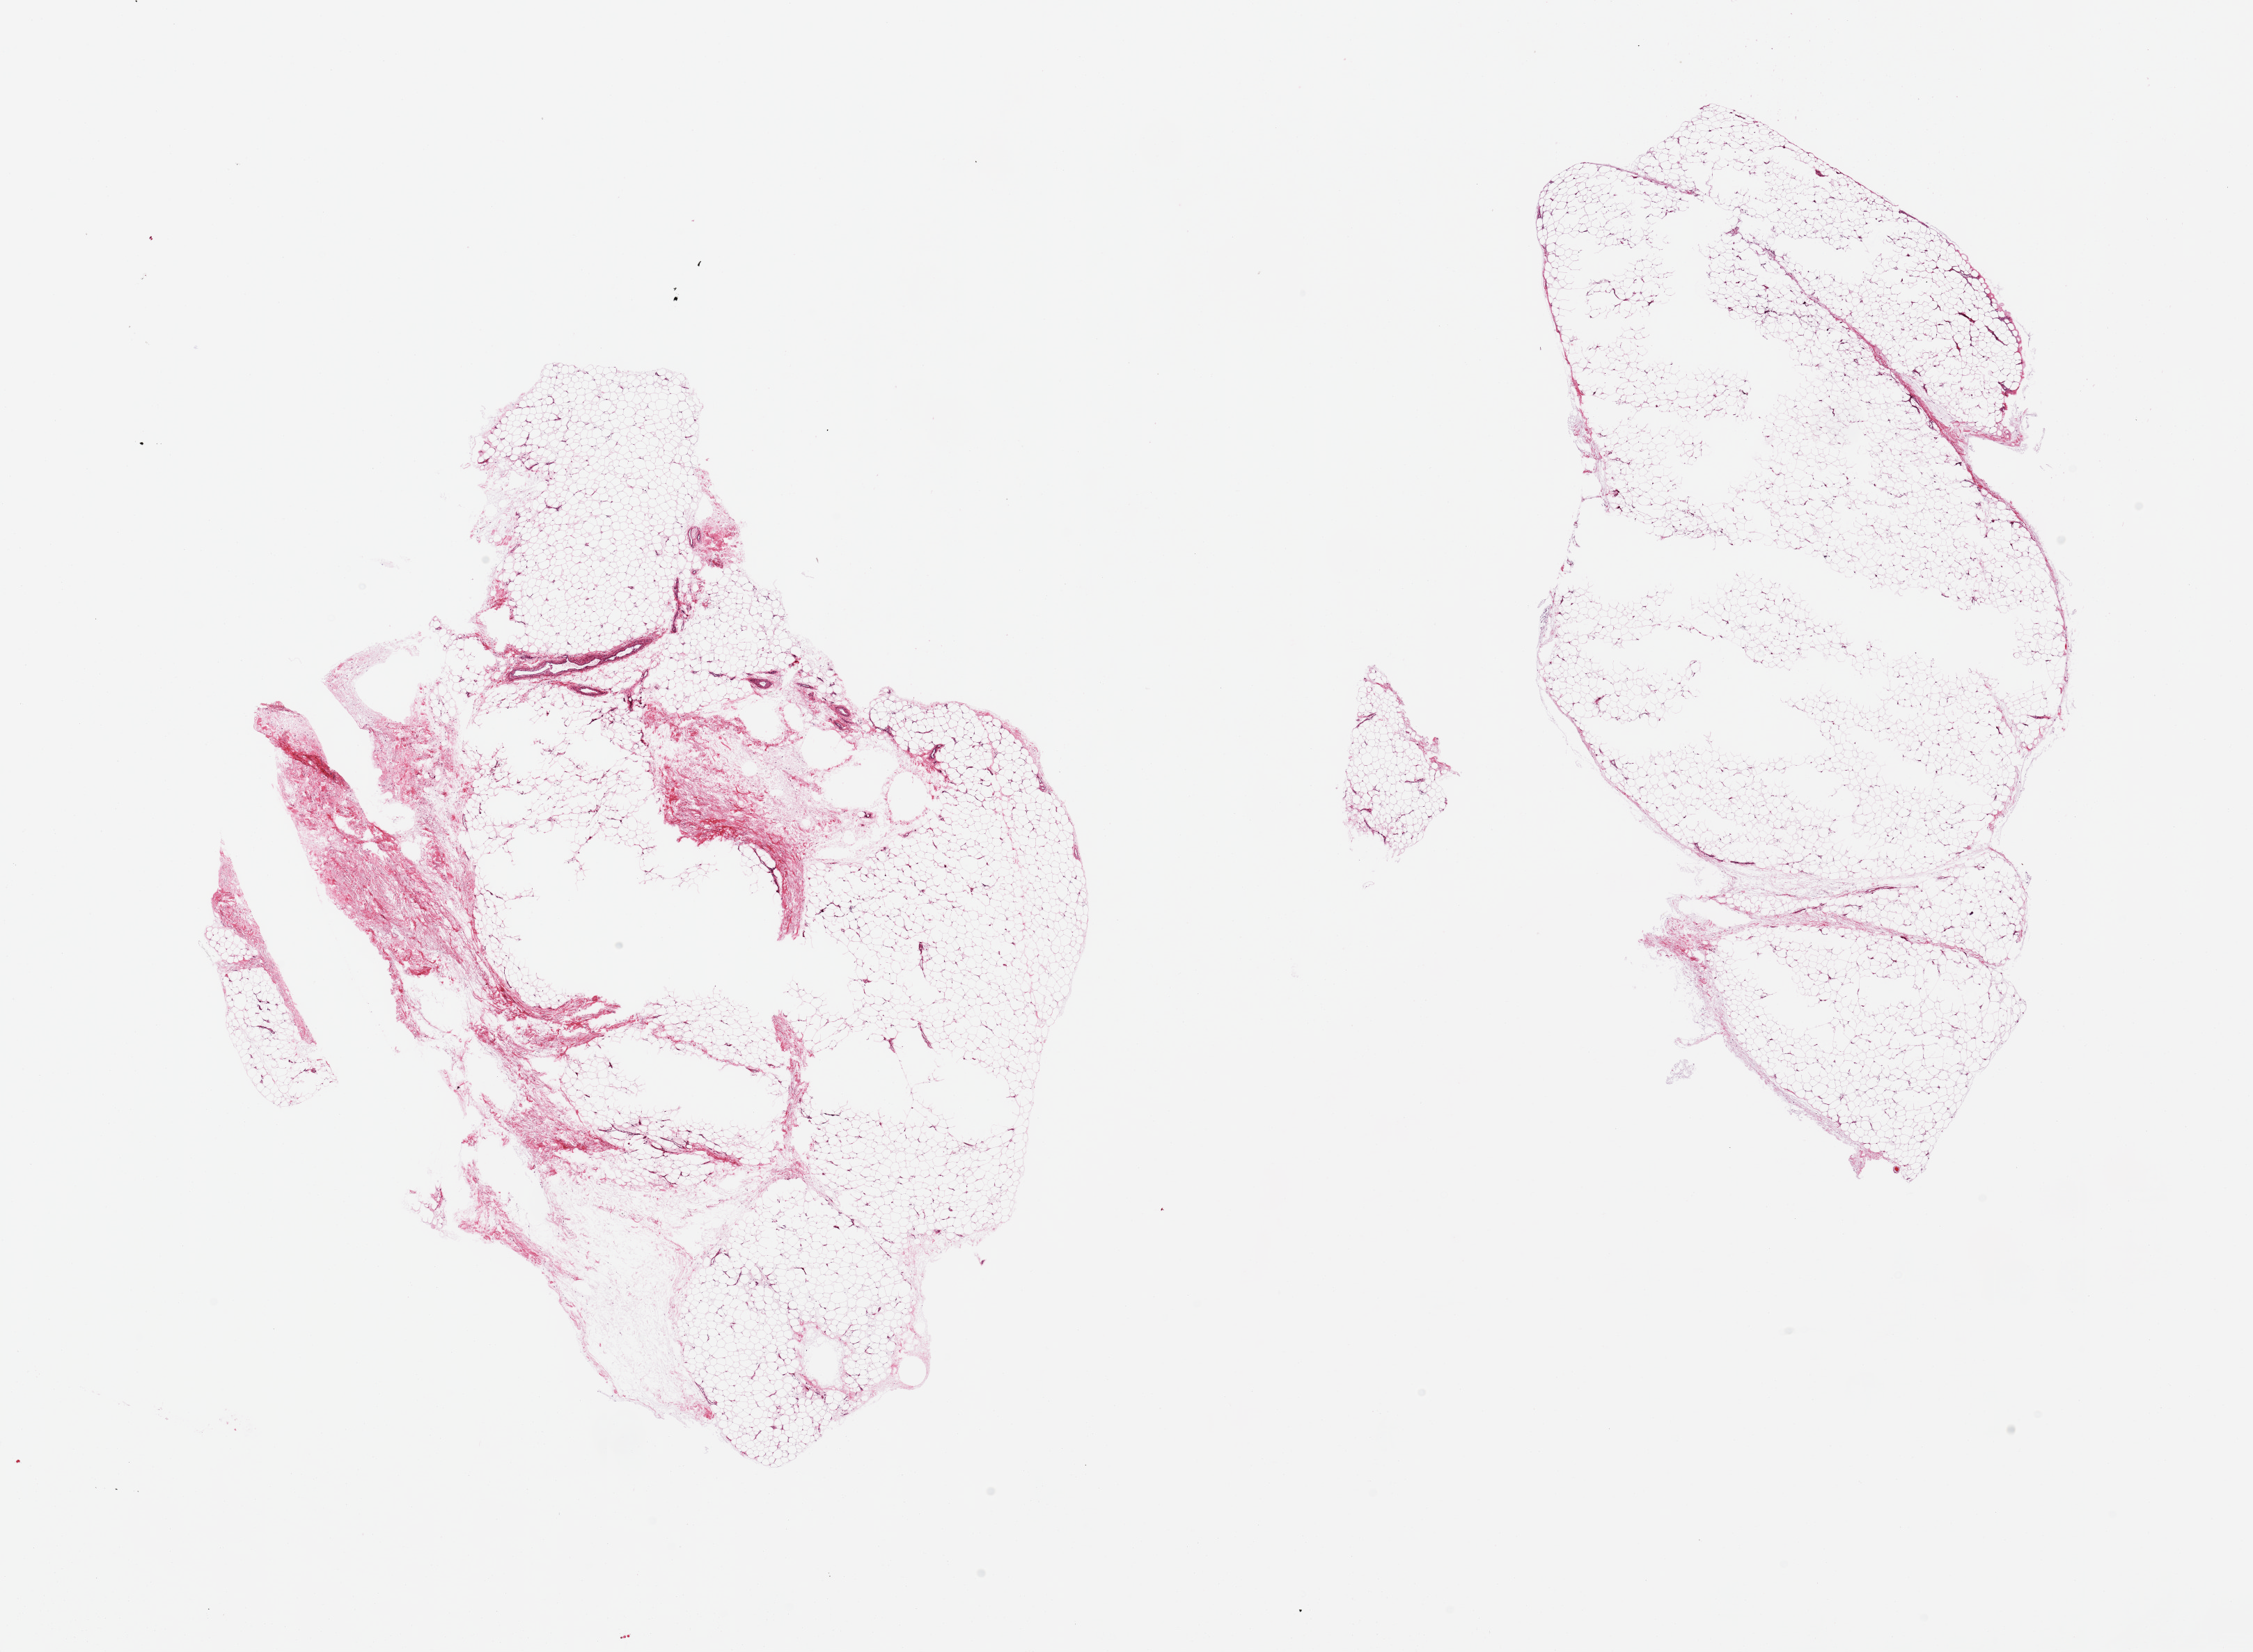
H&E whole-slide image — low-resolution overview of the scanned area, about 25.6 x 18.8 mm, PAXgene-fixed paraffin-embedded (PFPE) section, target tissue: adipose tissue, tissue donor sample. Donor: male.
Review note (as recorded): 2 pieces; 10% fibrous content.